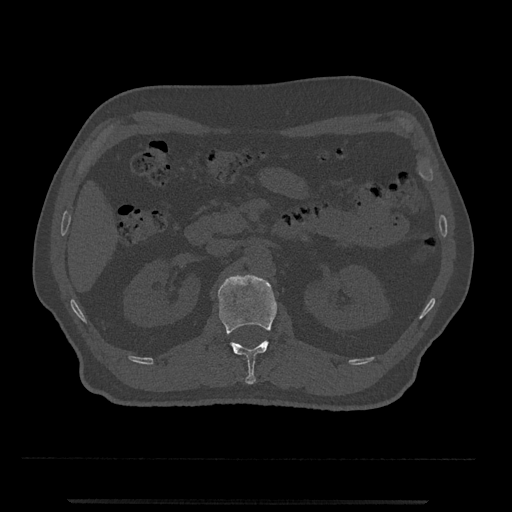
CT including the spine, one axial slice; bone window (W 1800 / L 400 HU); 0.5 mm slice thickness; 512 × 512 image matrix. Male patient, age 63 years. Case-level facts recorded for this patient, not image findings: primary cancer: prostate.
Outlined on this slice (semi-automatic segmentation, software-assisted and operator-edited):
- L1 vertebra: box from (x=218, y=274) to (x=277, y=385) px